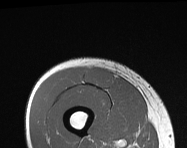
MRI of an extremity soft-tissue mass, one axial slice; position 40 of 114 along the scan axis; MR volume resampled by the dataset authors to the PET/CT grid (not the native acquisition matrix); 3.27 mm slice thickness; 187 × 148 image matrix, field of view 183 × 145 mm. Male patient. Case-level facts recorded for this patient, not image findings: histological type: pleiomorphic leiomyosarcoma; grade: intermediate; site of the primary tumour: right thigh.
Structures marked on this image (expert contour drawn on MRI and transferred to this co-registered scan by the dataset authors):
- gross tumour volume including surrounding oedema: box from (x=84, y=68) to (x=112, y=87) px